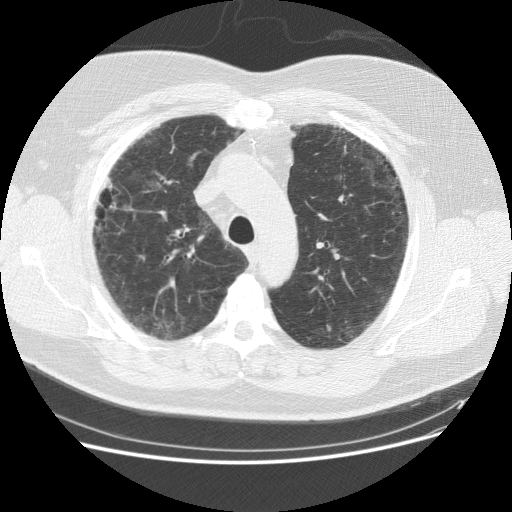
Axial slice from a low-dose chest CT screening exam; first (baseline) screen; lung window (W 1500 / L -600 HU); 2.5 mm slice thickness; standard (soft-tissue) reconstruction kernel (STANDARD). Male participant, aged 59 years at enrolment.
Expert reader's lesion annotation, bounding box [x1, y1, x2, y2] px = [82, 162, 139, 236]. The screening reader recorded 2 non-calcified nodules or masses ≥4 mm on this exam (right middle lobe, right lower lobe); which of them this box marks is not recorded. Official screen result: positive, change unspecified: nodule(s) >= 4 mm or enlarging nodule(s), mass(es), or other non-specific abnormalities suspicious for lung cancer. Lung cancer was diagnosed 338 days after this screen: adenocarcinoma, NOS, right upper lobe, right middle lobe, moderately differentiated (G2), stage IA (AJCC 6th edition), 13 mm at pathology.